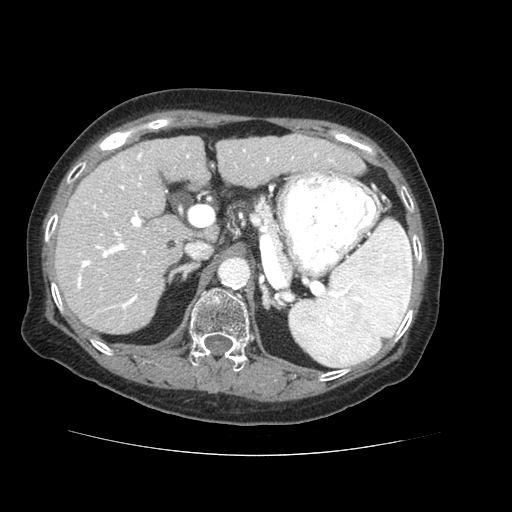
Contrast-enhanced abdominal CT (liver protocol), one axial slice; slice 35 of 73 in the series (ordered by position); reconstruction kernel STANDARD; soft-tissue window (W 400 / L 40 HU); 2.5 mm slice thickness; 512 × 512 image matrix. Case-level facts recorded for this patient, not image findings: diagnosis: hepatocellular carcinoma (patient treated with transarterial chemoembolisation; whether this scan precedes or follows treatment is not stated here); TNM stage (as recorded): Stage-IVB; Child-Pugh class: A; tumour differentiation: well differentiated; tumour nodularity: uninodular.
Structures marked on this image (semi-automatically segmented with operator editing):
- liver parenchyma outside the tumour (the mass and vessels are separate outlines, so this box may not span the whole liver): bounding box (x1, y1, x2, y2) in pixels: (54, 134, 364, 334)
- liver vessels: (77, 149, 334, 311)